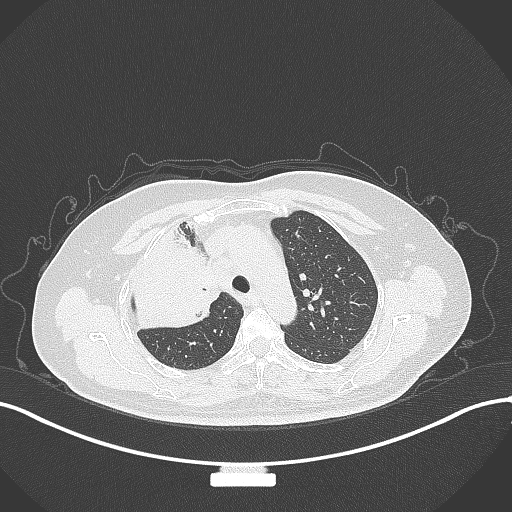
Chest CT, one axial slice; position 226 of 309 along the scan axis; reconstruction kernel B70f; 120 kVp; lung window (W 1500 / L -600 HU); 1 mm slice thickness; 512 × 512 image matrix, field of view 400 × 400 mm. Female patient, age 60 years. From the clinical record (not read from this slice): clinical TNM (as recorded): T3 N1 M1.
Outlined on this slice (rectangle marked by the reading radiologist):
- lung tumour (recorded histology: adenocarcinoma): bounding box [x1, y1, x2, y2] px = [128, 227, 225, 338]